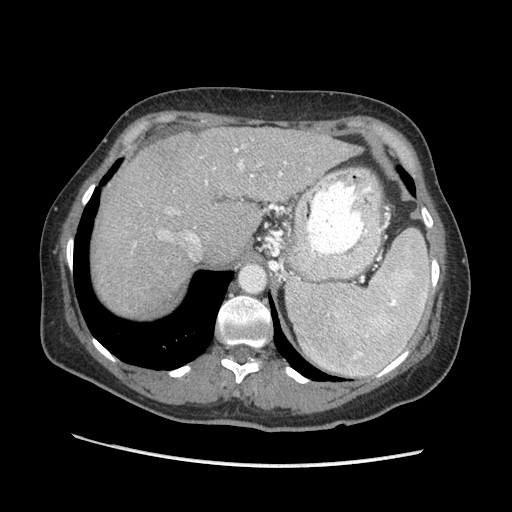
Contrast-enhanced abdominal CT (liver protocol), one axial slice. Position 144 of 170 along the scan axis. 140 kVp. Soft-tissue window (W 400 / L 40 HU). 2.5 mm slice thickness. 512 × 512 image matrix. From the clinical record (not read from this slice): diagnosis: hepatocellular carcinoma (patient treated with transarterial chemoembolisation; whether this scan precedes or follows treatment is not stated here); TNM stage (as recorded): Stage-II; Child-Pugh class: A; tumour differentiation: no biopsy; tumour nodularity: multinodular.
Outlined on this slice (semi-automatically segmented with operator editing):
- abdominal aorta: bounding box (x1, y1, x2, y2) in pixels: (240, 265, 265, 292)
- liver parenchyma outside the tumour (the mass and vessels are separate outlines, so this box may not span the whole liver): (96, 126, 359, 316)
- liver vessels: (134, 145, 310, 257)